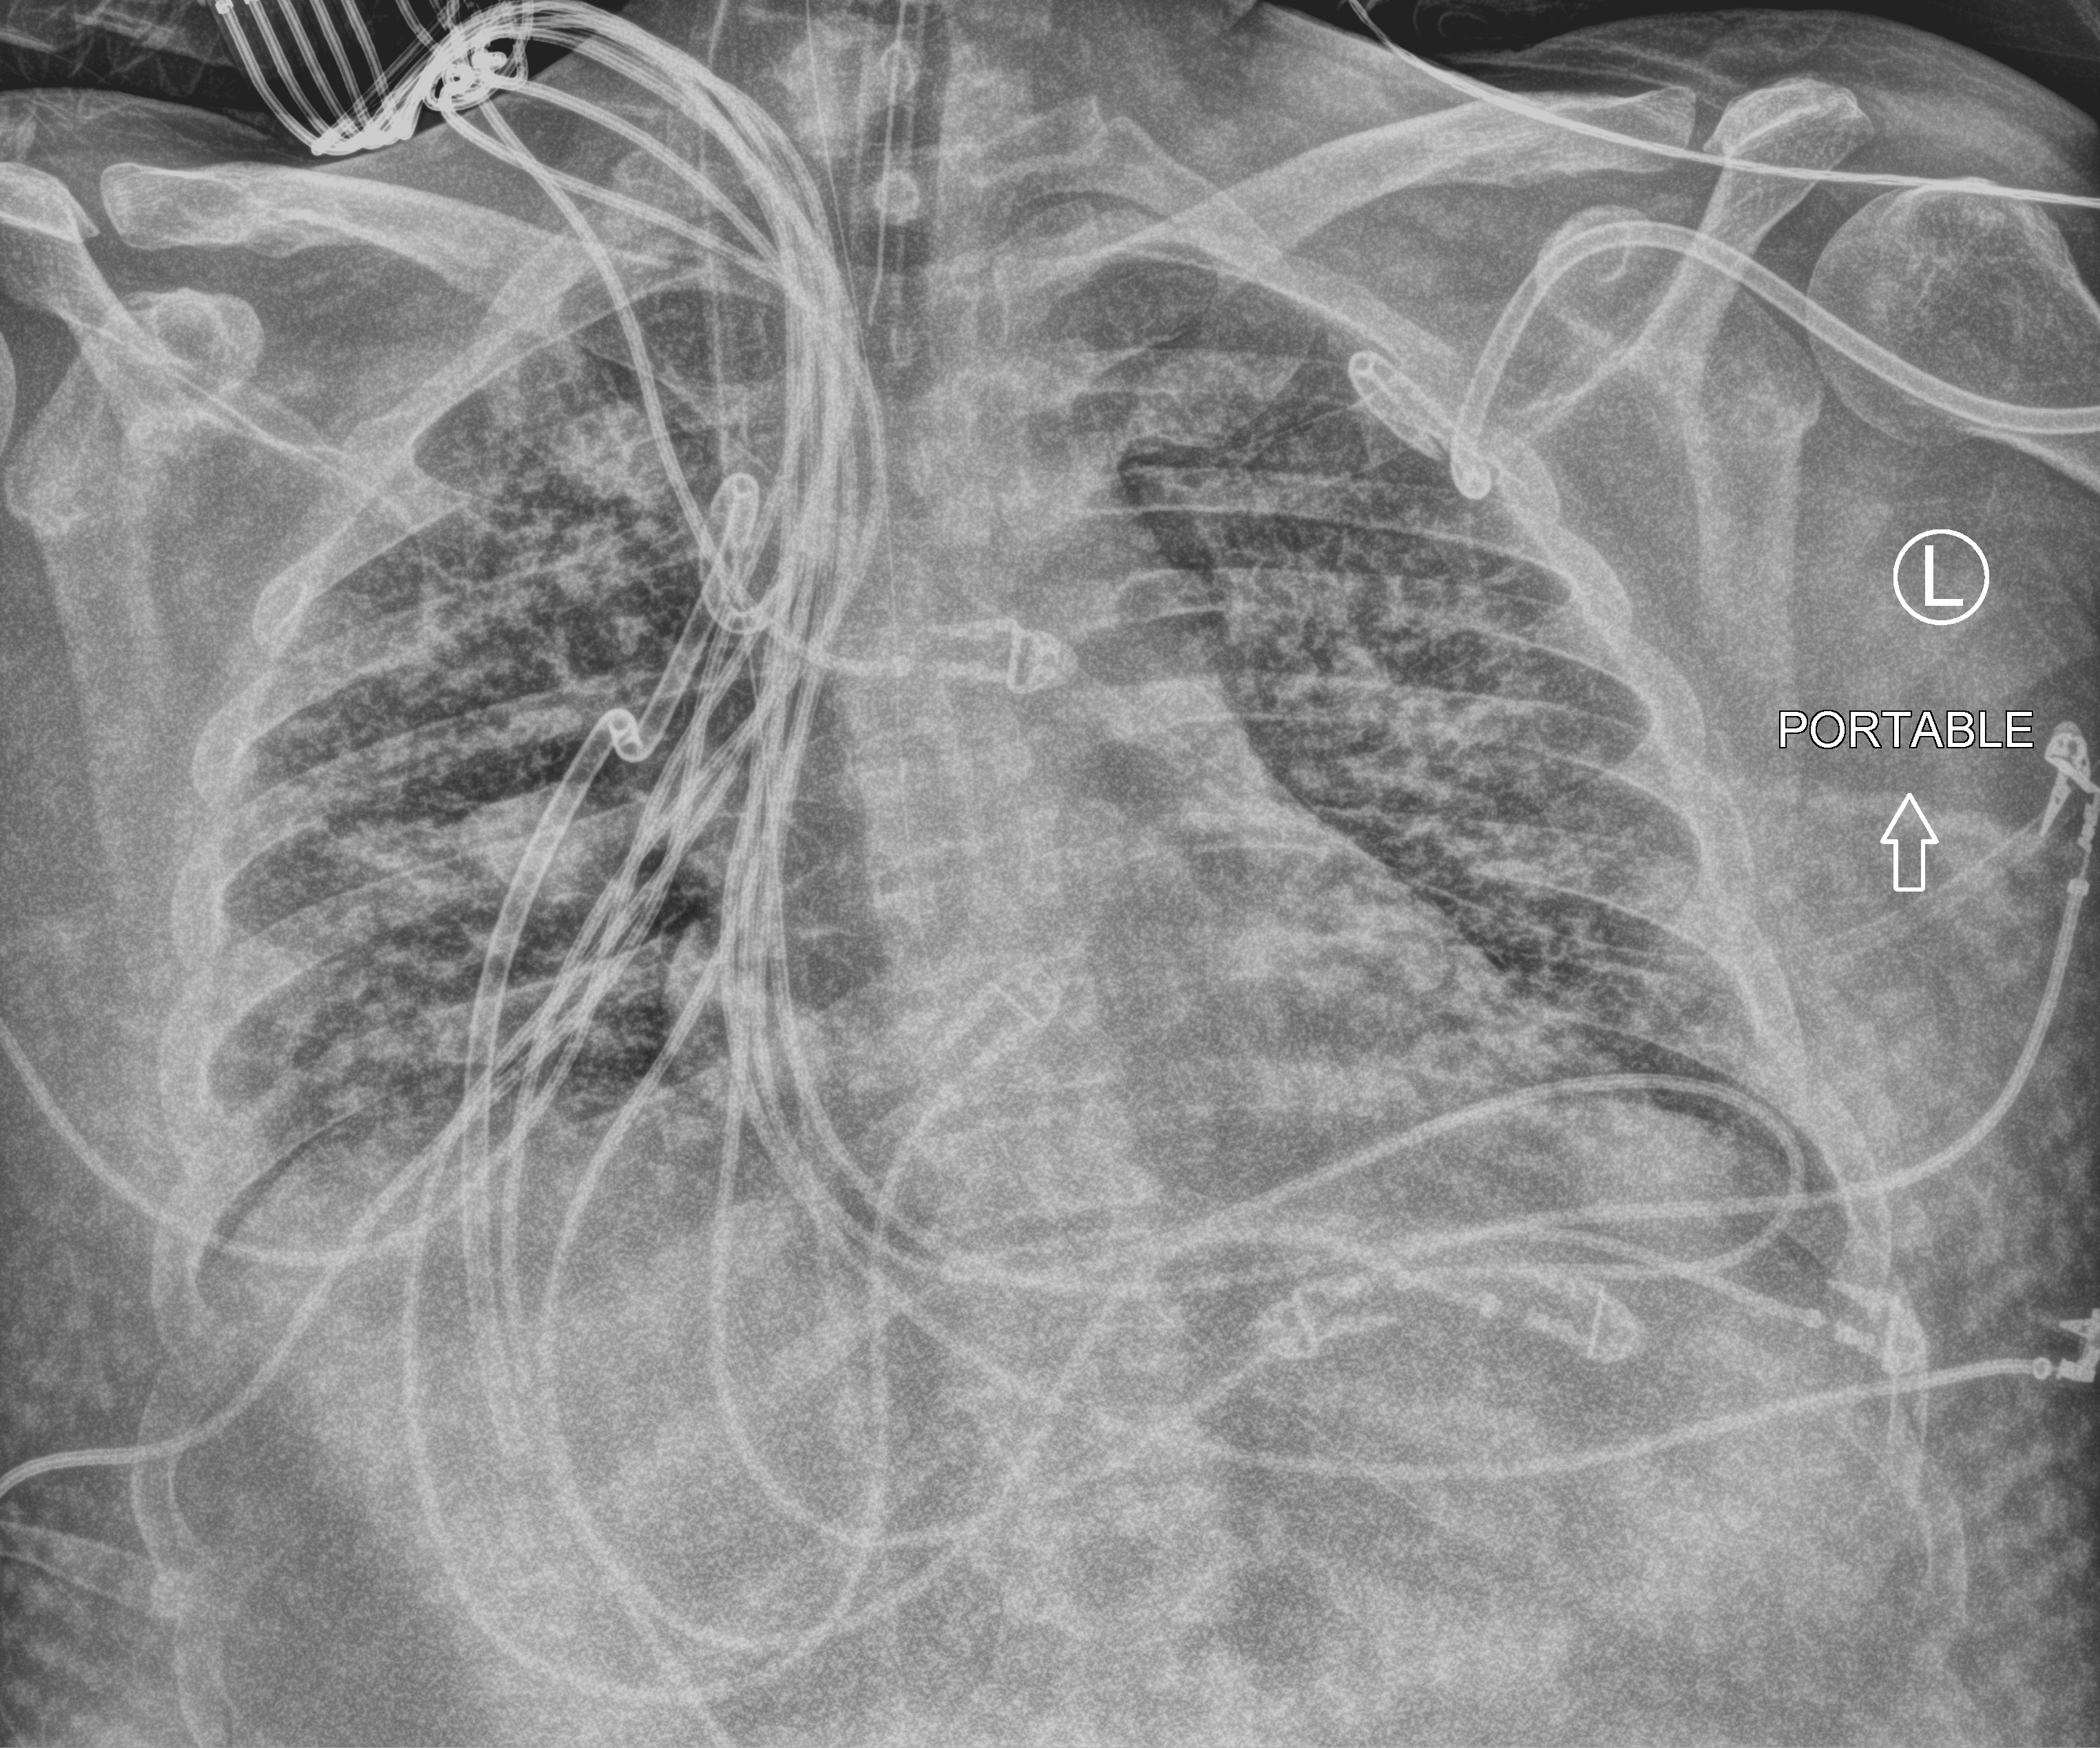
Chest X-ray (portable), anteroposterior (AP) projection. Adult patient hospitalised with COVID-19, age 18–59 years.
Admission-level facts for this patient (not findings on this image; timing relative to this image not recorded):
- admitted to intensive care during this hospital stay: yes